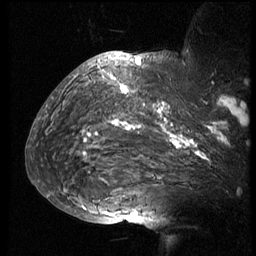
Breast MRI (dynamic contrast-enhanced), one sagittal slice. Slice 52 of 74 in the series (ordered by position). 3 images stored at this slice position (order not interpretable as contrast timing). 1.5 T. TE 4.2 ms, TR 8.9 ms. 2.5 mm slice thickness. 256 × 256 image matrix, field of view 200 × 200 mm. Patient: female, 57 years. Case-level facts recorded for this patient, not image findings: setting: breast cancer imaged before/during neoadjuvant chemotherapy; receptor status: HER2-positive.
Annotated regions visible in this slice (semi-automatic segmentation, software-assisted and operator-edited):
- analysis volume of interest (the breast-tissue region the enhancement analysis was run in; not a lesion): bounding box [x1, y1, x2, y2] px = [51, 67, 249, 173]
- tumour enhancement mask (voxels above the 140 % enhancement threshold inside the analysis volume of interest): [83, 77, 247, 160]